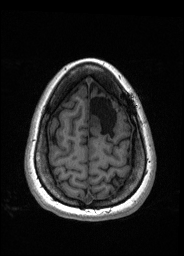
Pre-operative brain MRI before brain-tumour surgery, one axial slice. Position 42 of 176 along the scan axis. T1-weighted post-contrast. 1 mm slice thickness. 184 × 256 image matrix, field of view 180 × 250 mm. Case-level facts recorded for this patient, not image findings: histopathology: Oligodendroglioma; WHO grade: 2; IDH mutation: yes; tumour location: Left Frontal.
Structures marked on this image (expert manual segmentation):
- tumour: box from (x=89, y=114) to (x=101, y=127) px